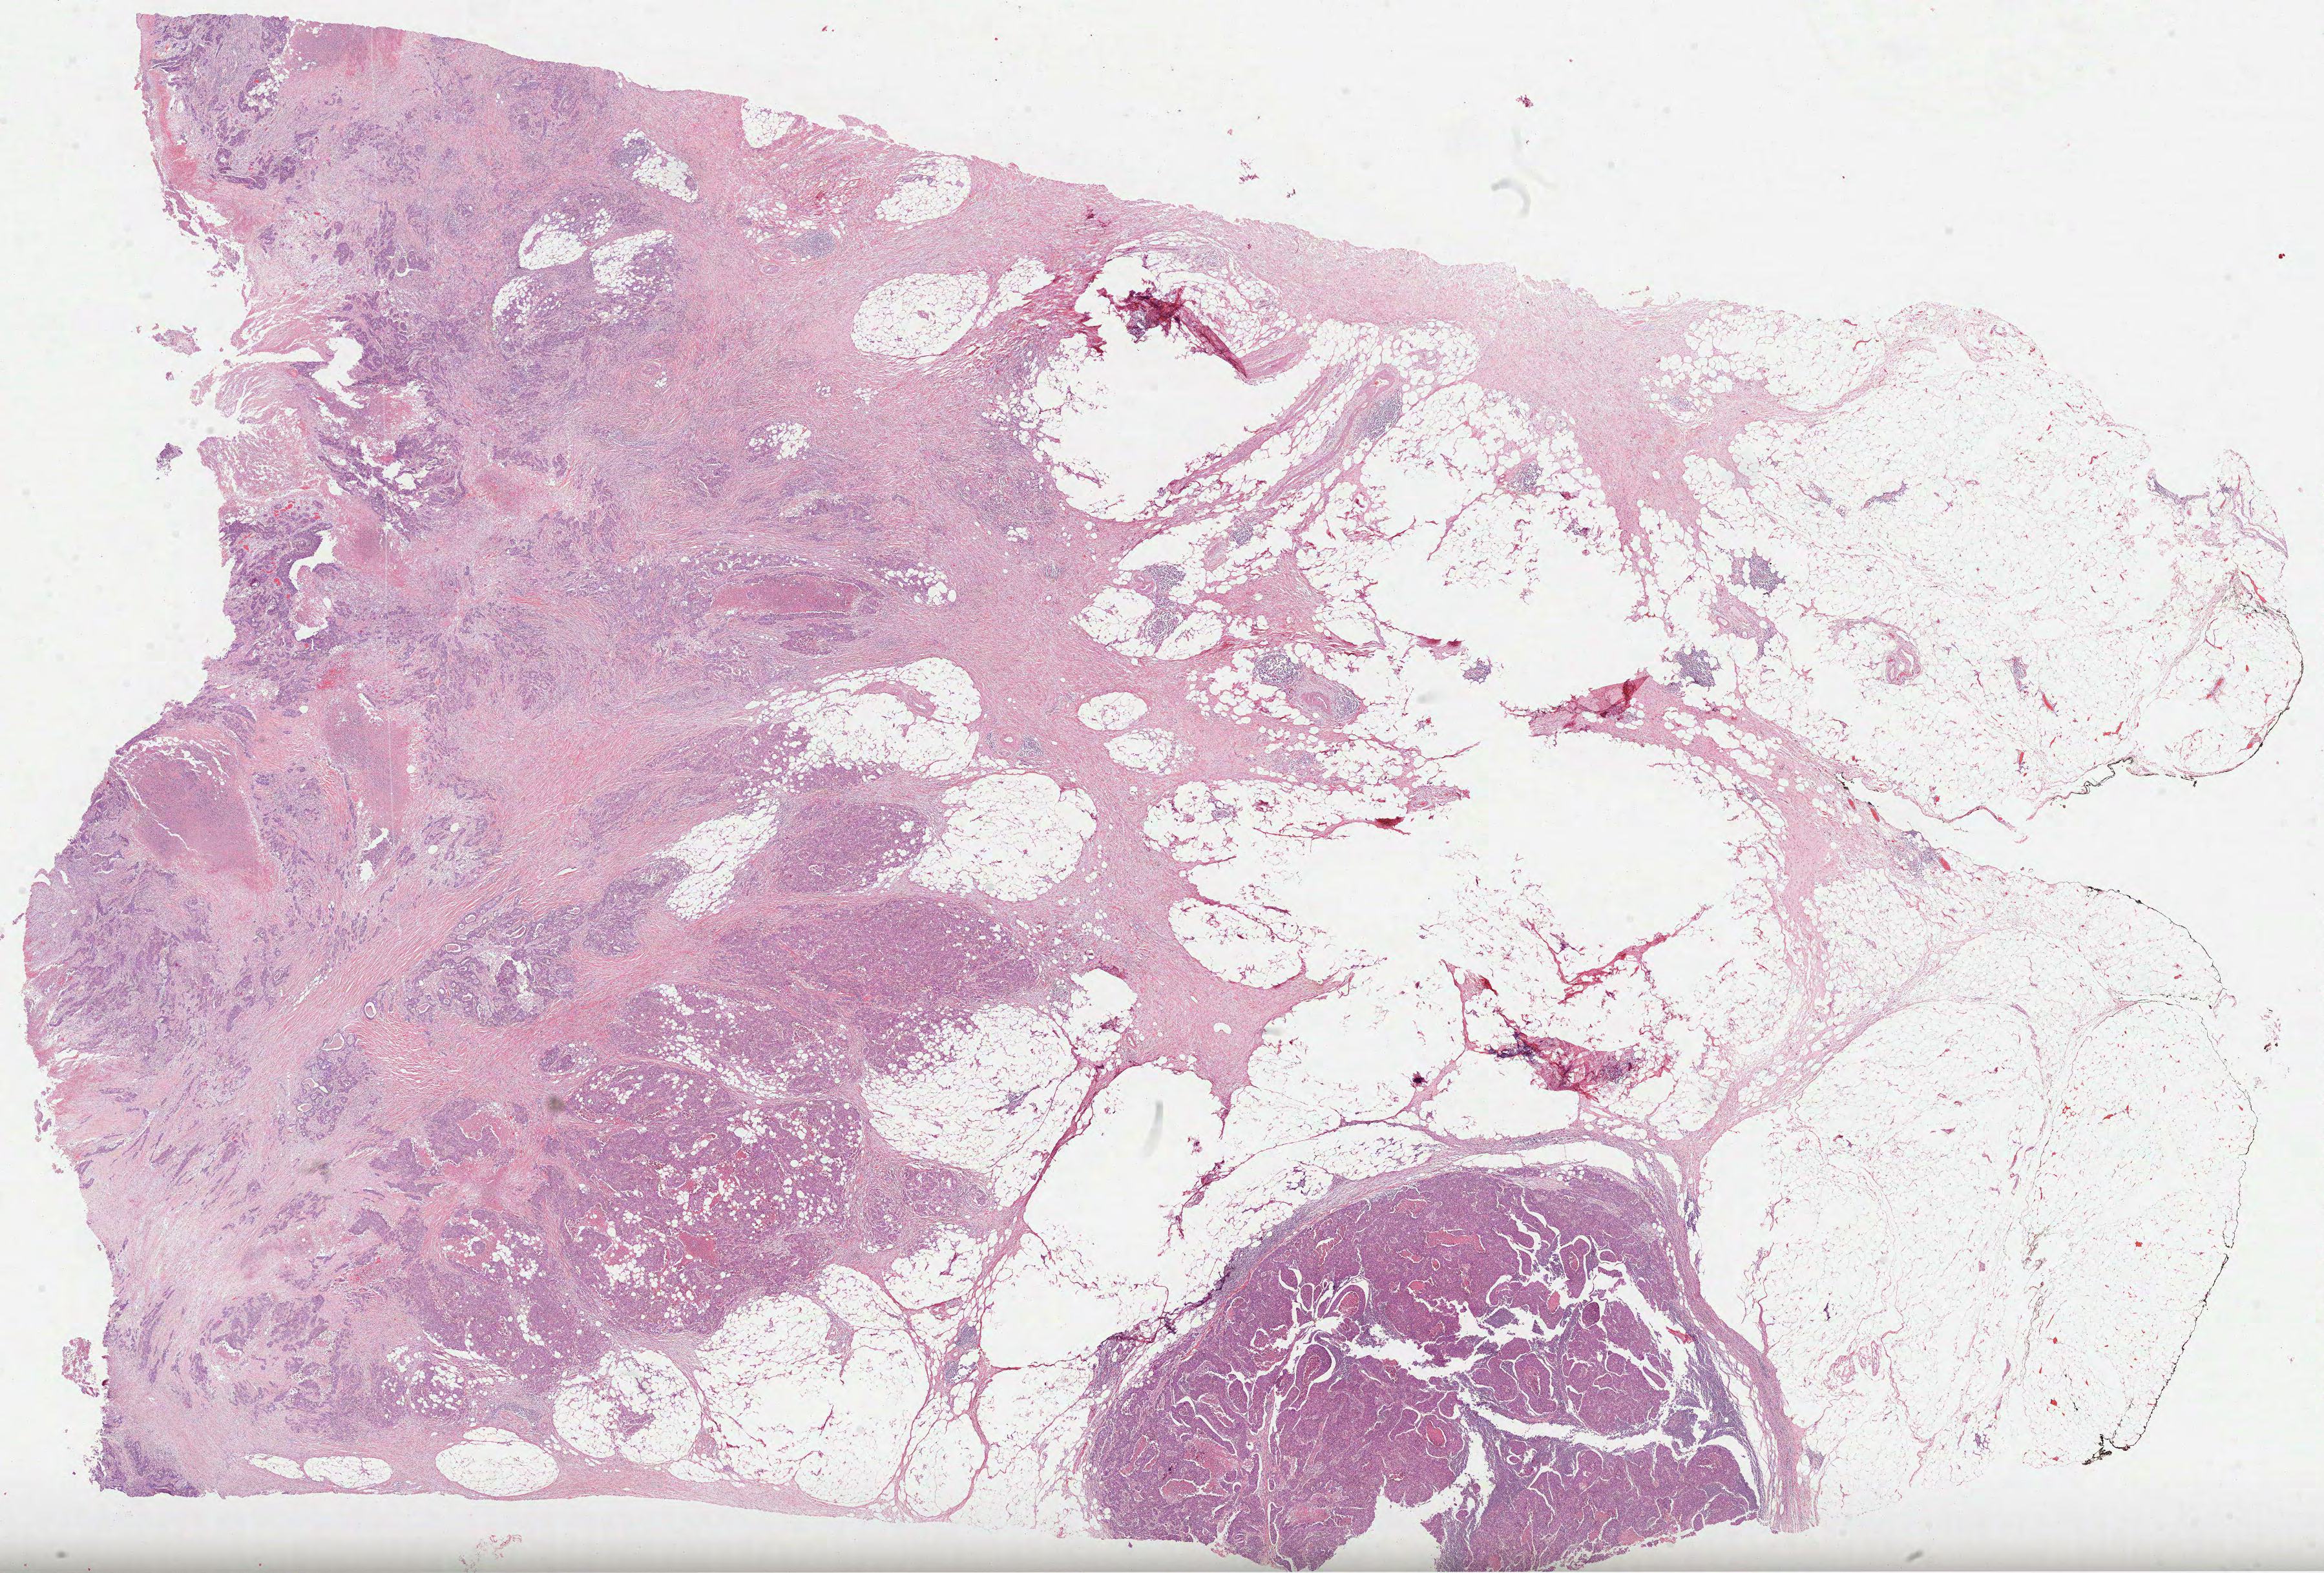
Whole-slide histology image, H&E-stained — low-resolution overview of the scanned area, about 29.0 x 19.6 mm (acquisition: 40x scan); formalin-fixed paraffin-embedded (FFPE) diagnostic section; primary tumour sample from the colon. Patient: male, age at initial diagnosis 69 years.
Pathologic diagnosis: Adenocarcinoma, NOS (descending colon). AJCC pathologic stage: IIIC (6th edition).